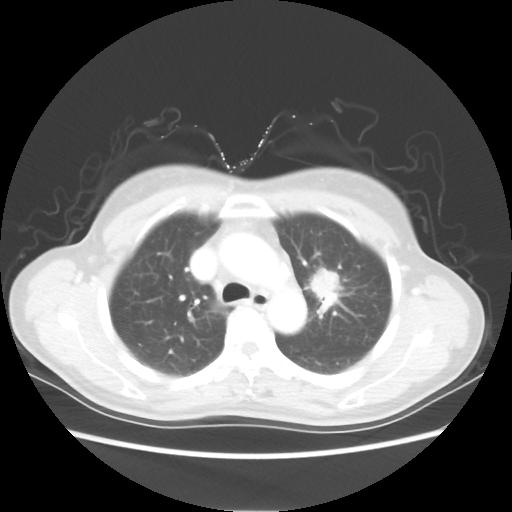
Chest CT, one axial slice; position 39 of 54 along the scan axis; reconstruction kernel STANDARD; lung window (W 1500 / L -600 HU); 5 mm slice thickness; 512 × 512 image matrix, field of view 360 × 360 mm. Patient: female, 53 years. Case-level facts recorded for this patient, not image findings: clinical TNM (as recorded): T1c N0 M0.
Outlined on this slice (bounding box drawn by a radiologist):
- lung tumour (recorded histology: adenocarcinoma): bounding box (x1, y1, x2, y2) in pixels: (309, 263, 342, 306)
- lung tumour (recorded histology: adenocarcinoma): (311, 265, 348, 304)